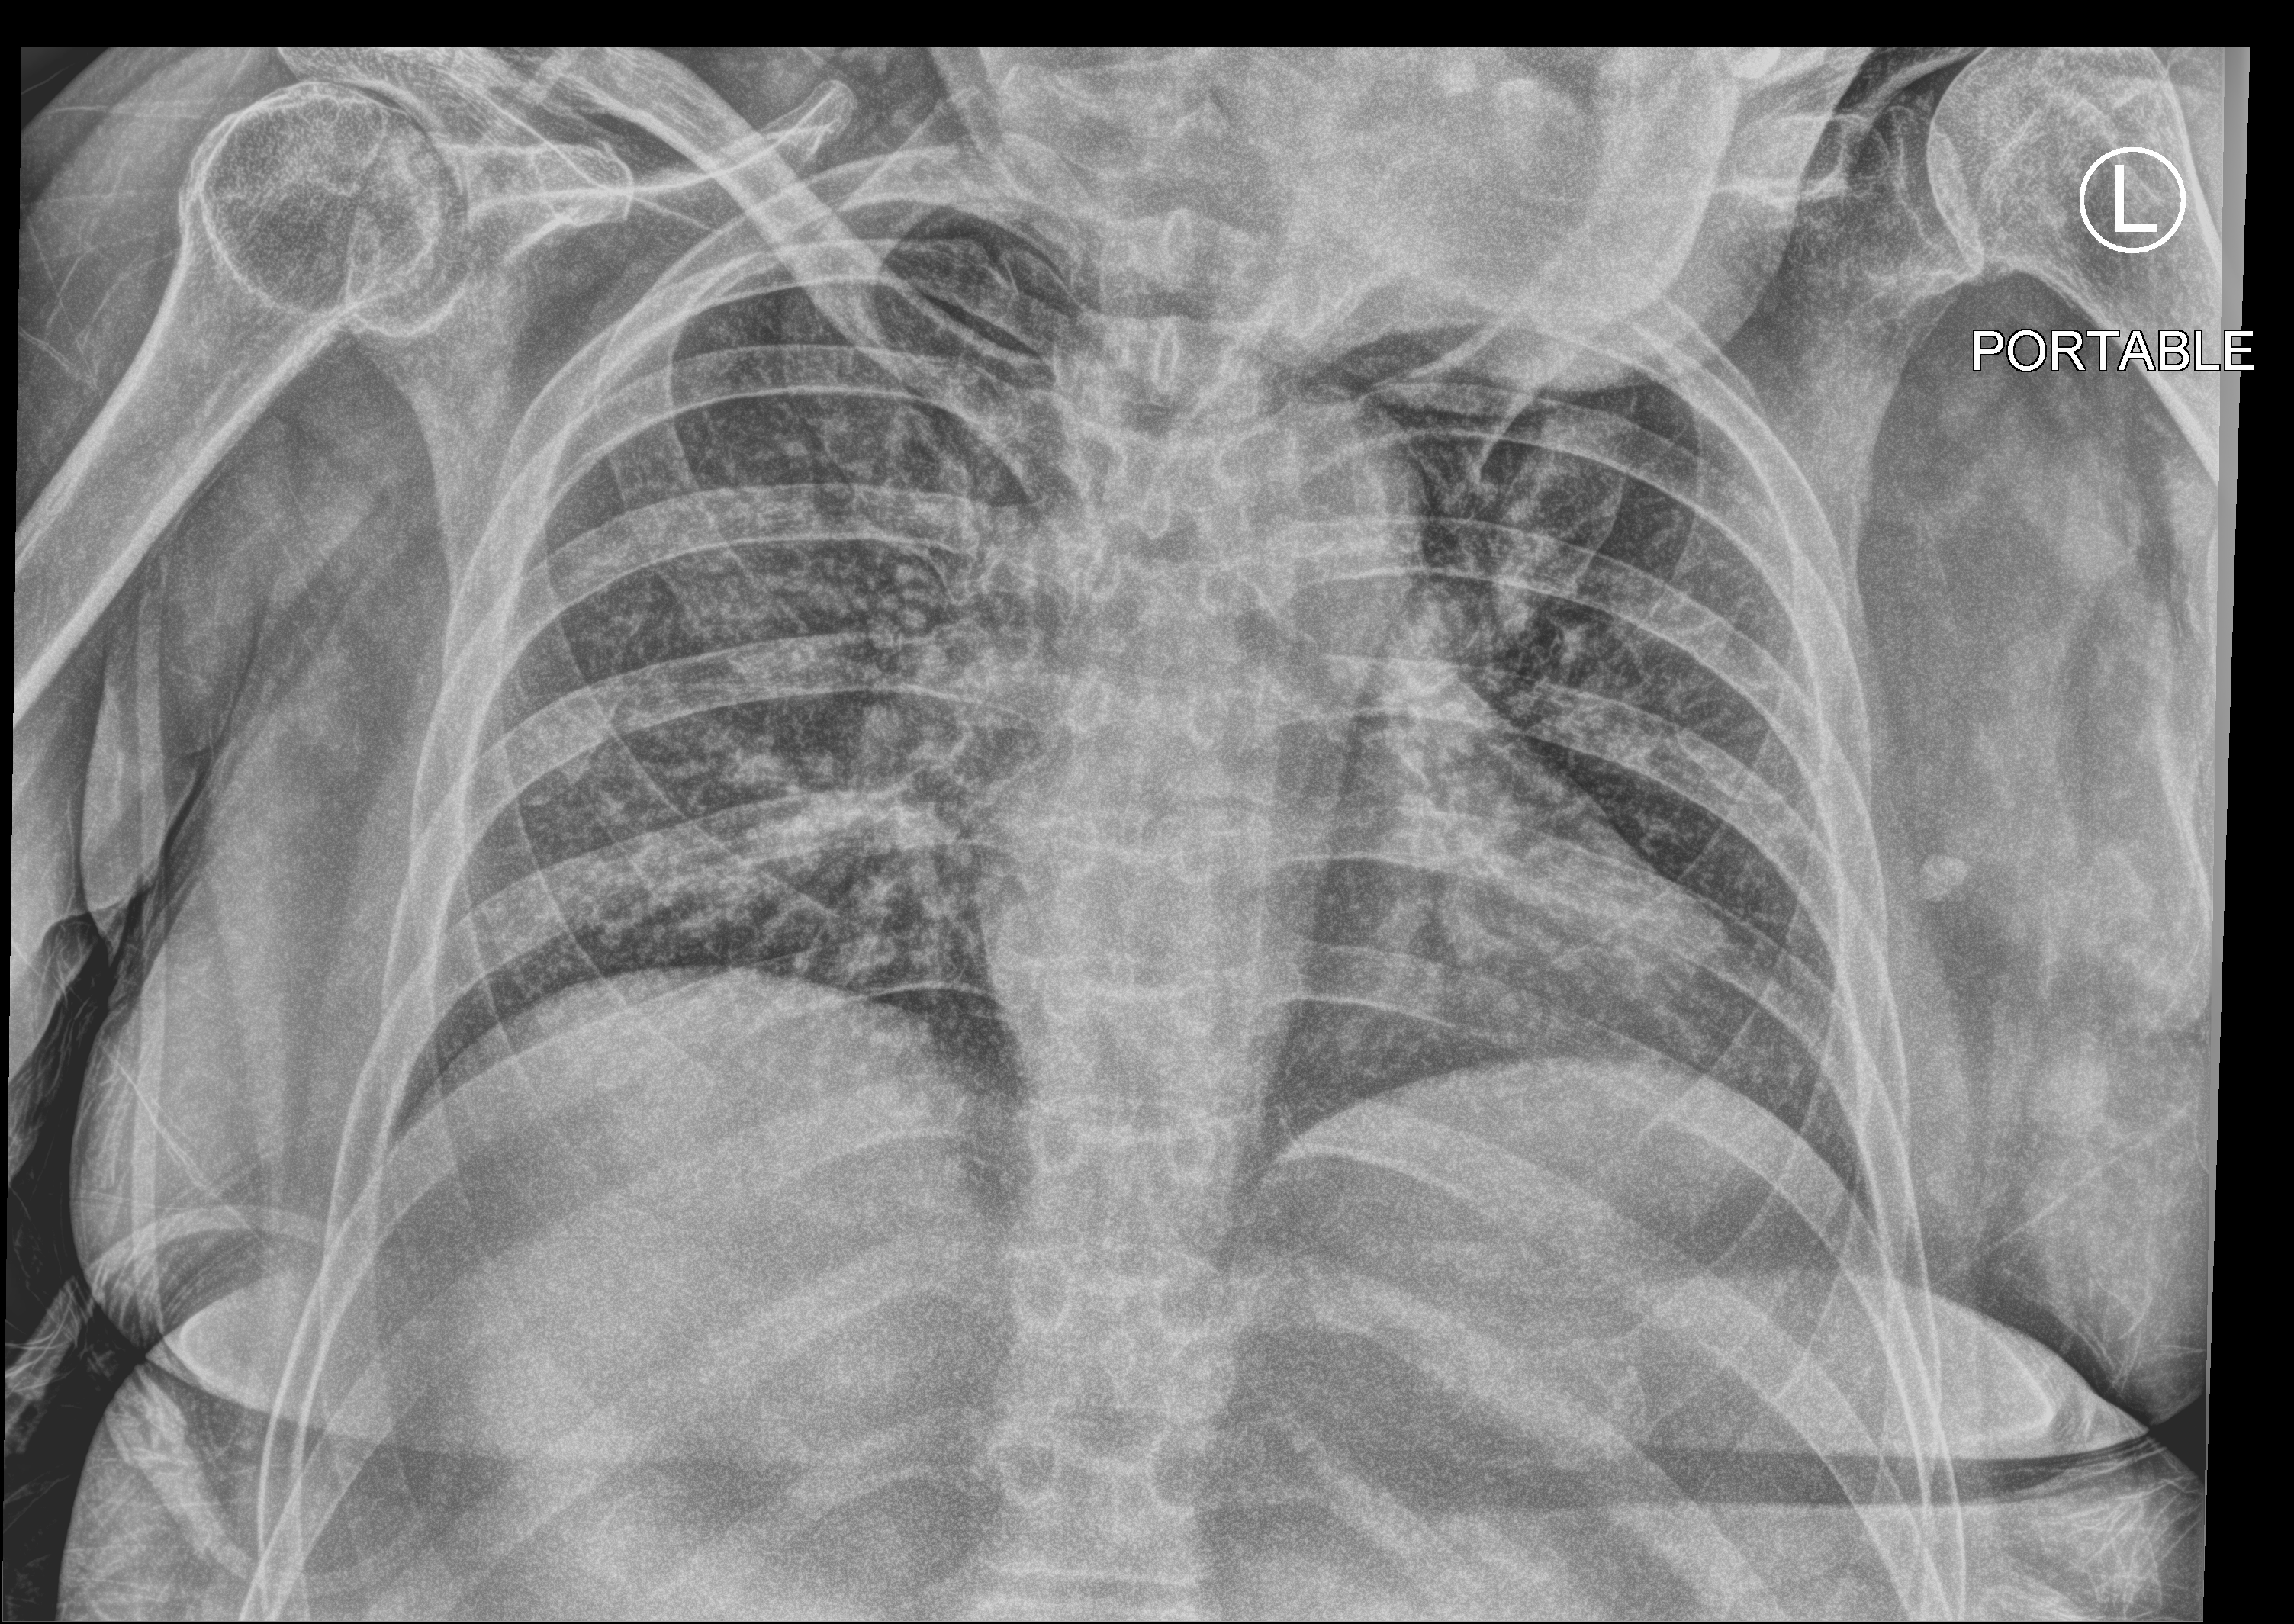
Portable chest radiograph; anteroposterior (AP) projection. Female patient hospitalised with COVID-19, age 60–74 years.
Hospital-stay facts (about this admission, not read from this image; timing relative to this image not recorded): mechanically ventilated during this hospital stay: no.